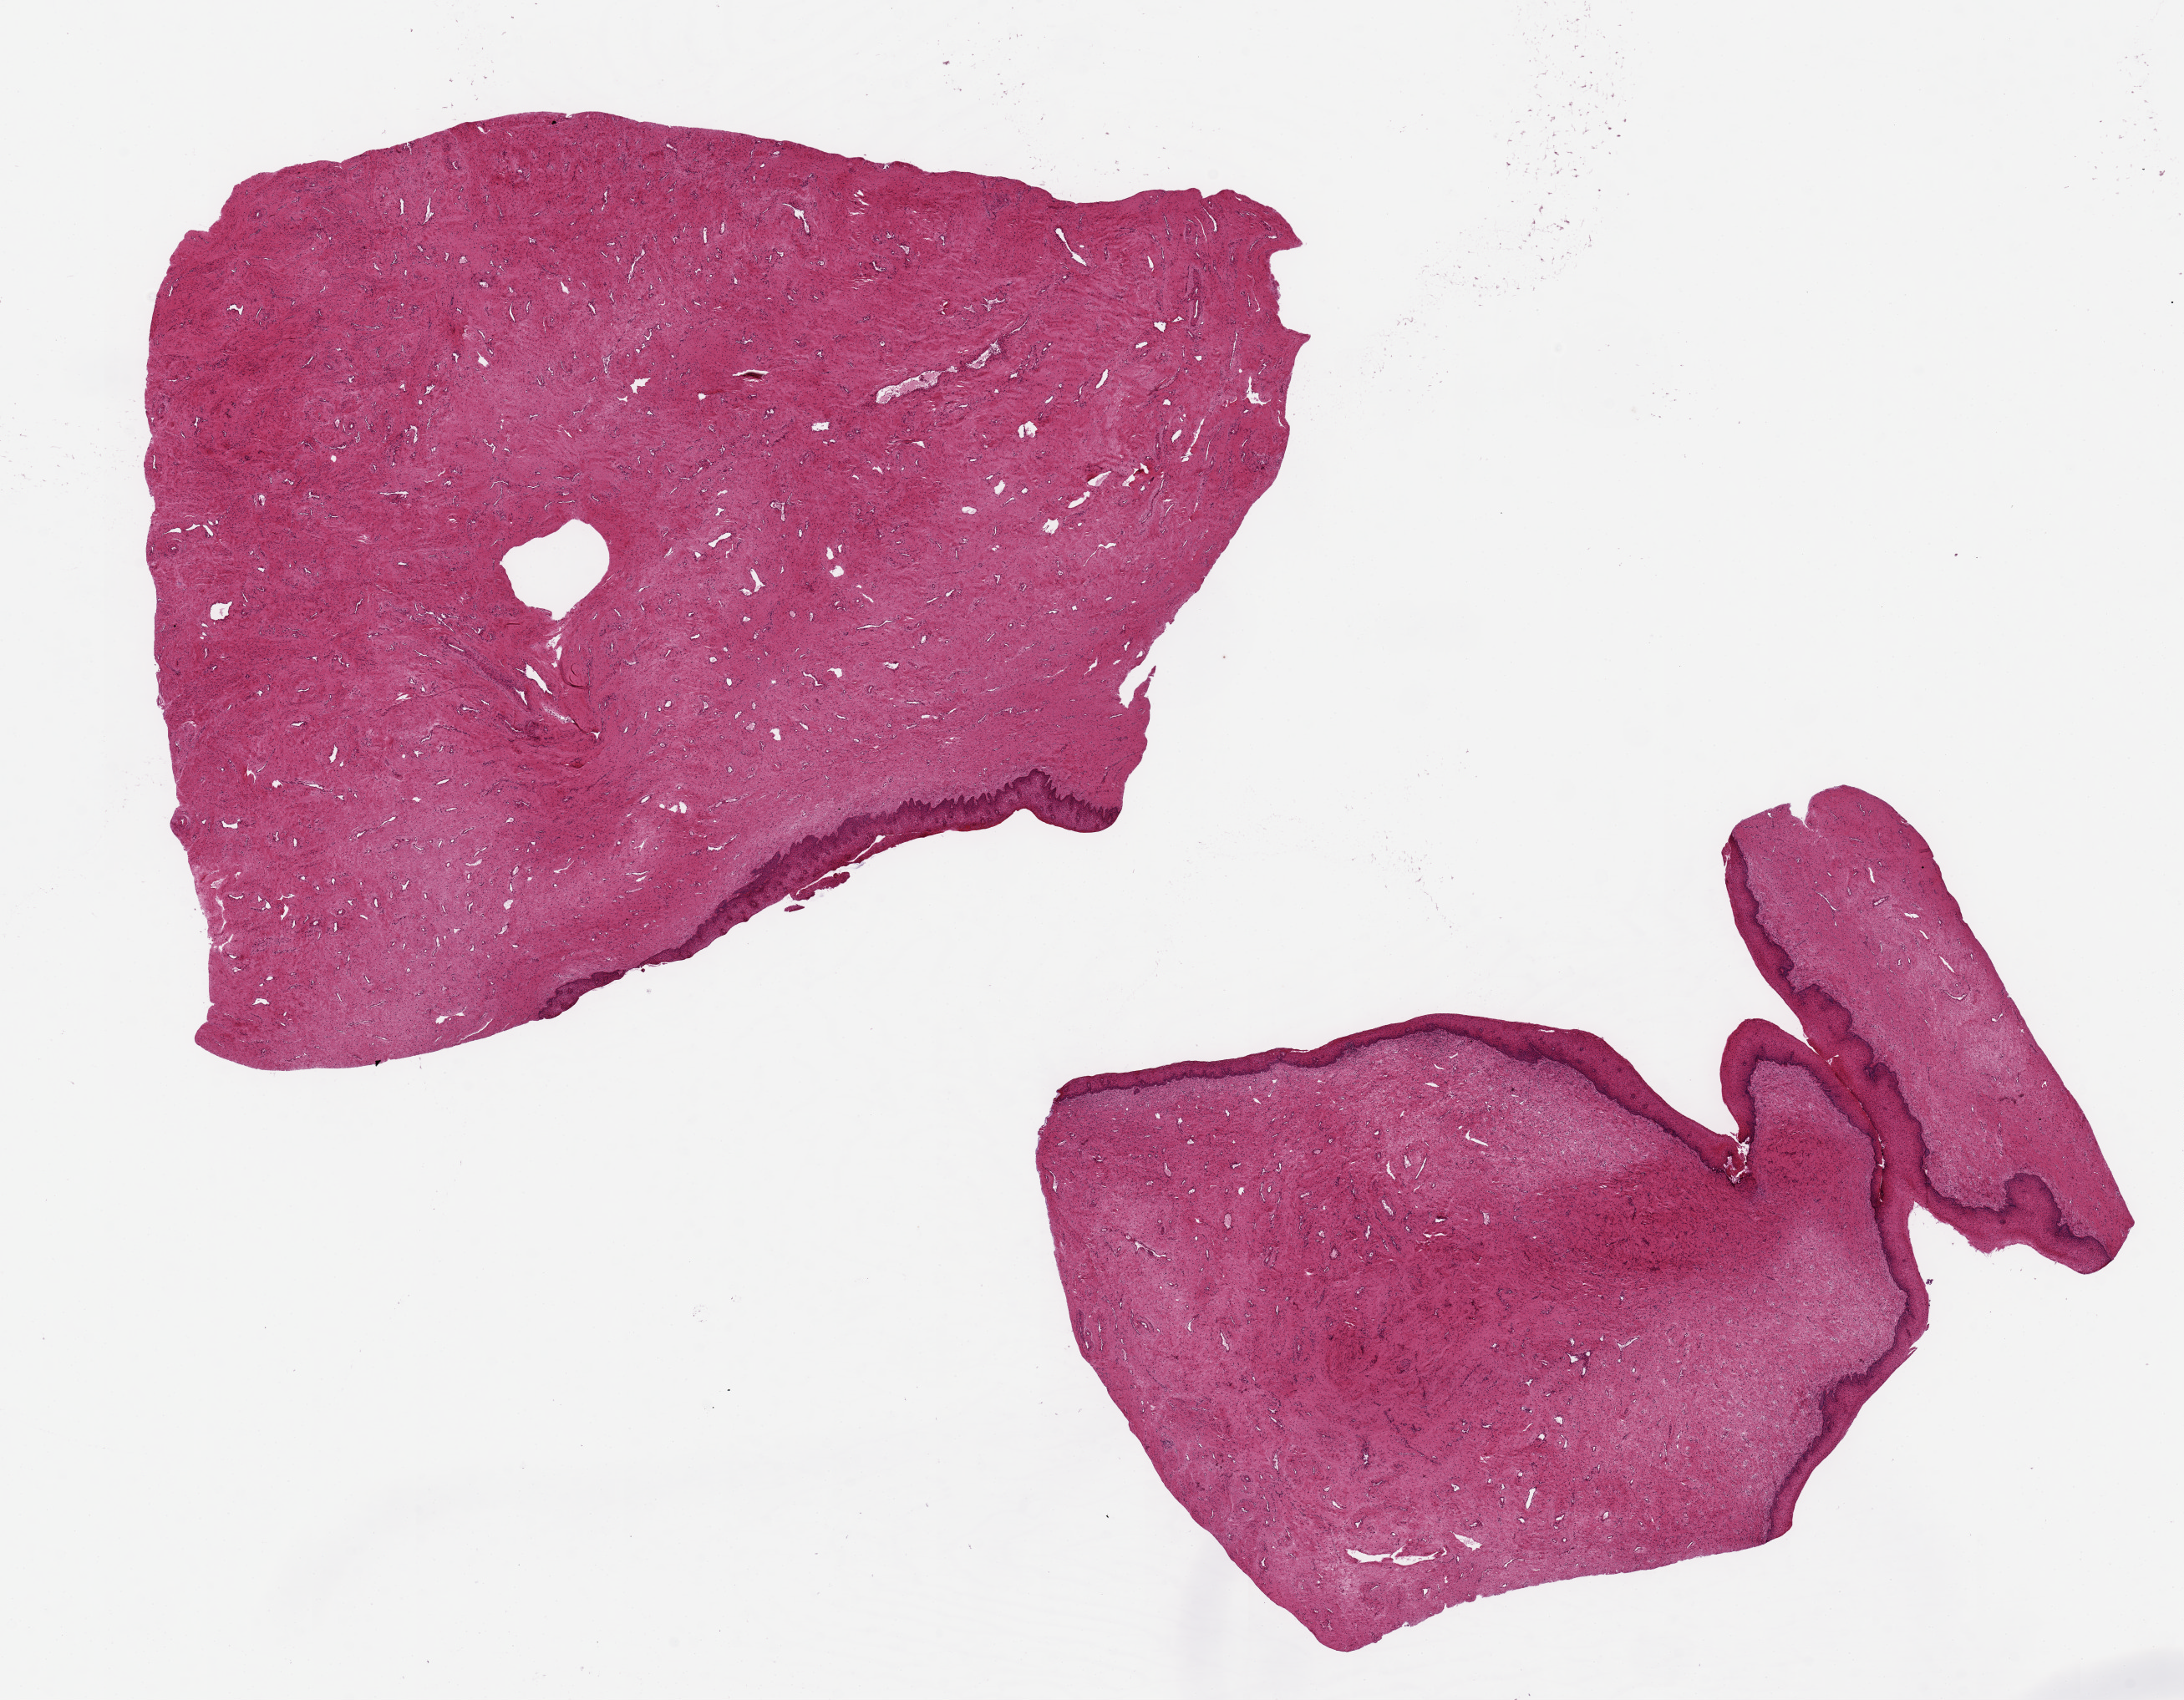
Whole-slide image, hematoxylin and eosin (H&E) stain — a low-resolution overview of the entire scanned area, about 20.7 x 16.1 mm (from a 20x scan). PAXgene-fixed paraffin-embedded (PFPE) section. Target tissue: exocervix. Tissue donor sample. Female donor.
* pathologist's review note for this sample: 2 pieces 9x6 & 11x8 mm; well preserved